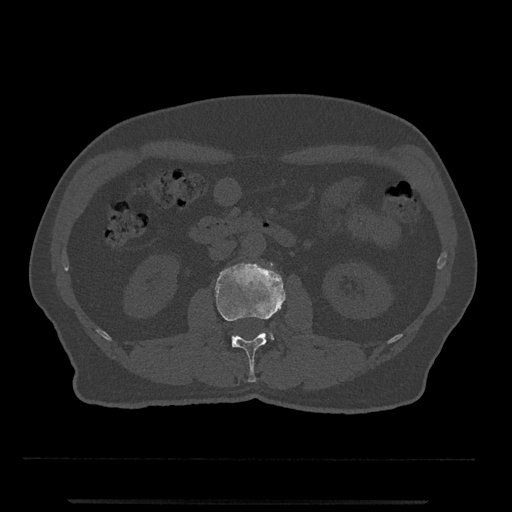
CT including the spine, one axial slice; slice 254 of 797 in the series (ordered by position); 120 kVp; bone window (W 1800 / L 400 HU); 0.5 mm slice thickness; 512 × 512 image matrix. Patient: male, 63 years. From the clinical record (not read from this slice): primary cancer: prostate.
Structures marked on this image (semi-automatically segmented with operator editing):
- L2 vertebra: bounding box [x1, y1, x2, y2] px = [215, 262, 286, 383]
- L3 vertebra: [270, 333, 273, 339]